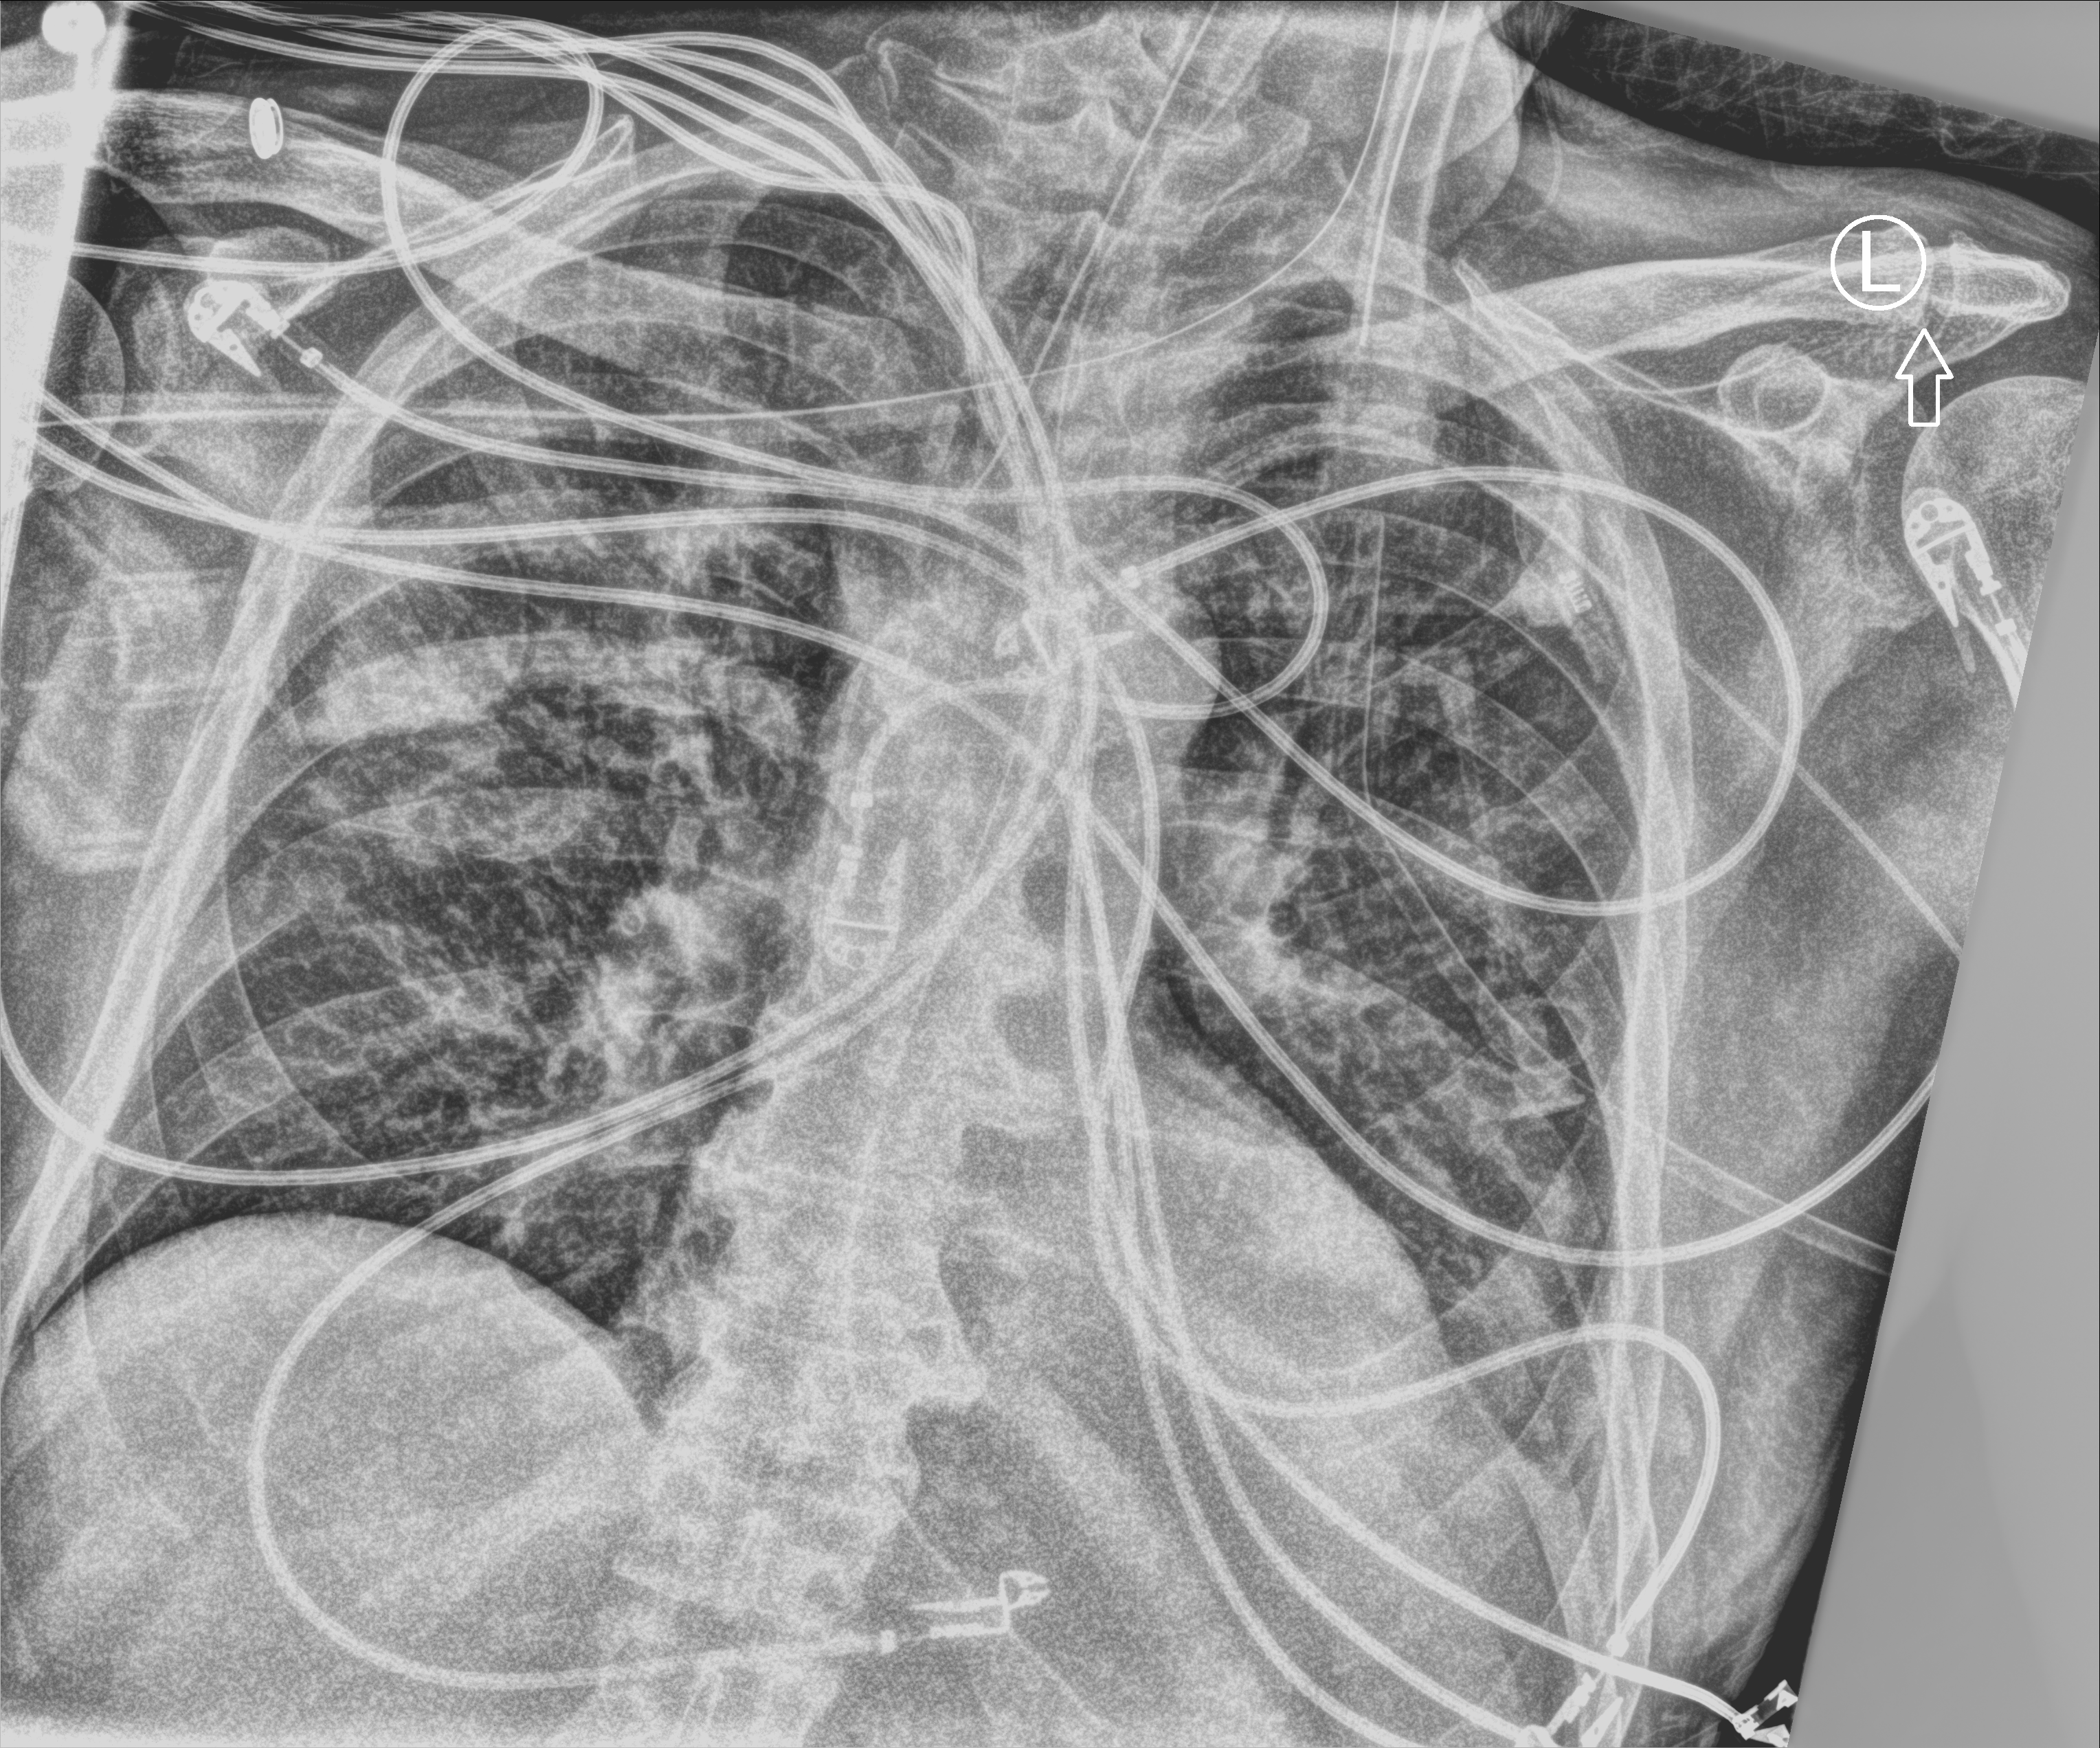
Bedside chest radiograph (computed radiography); anteroposterior (AP) projection. Patient hospitalised with COVID-19; male, aged 60–74 years.
Admission-level facts for this patient (not findings on this image; timing relative to this image not recorded): hypertension (admission record): yes.